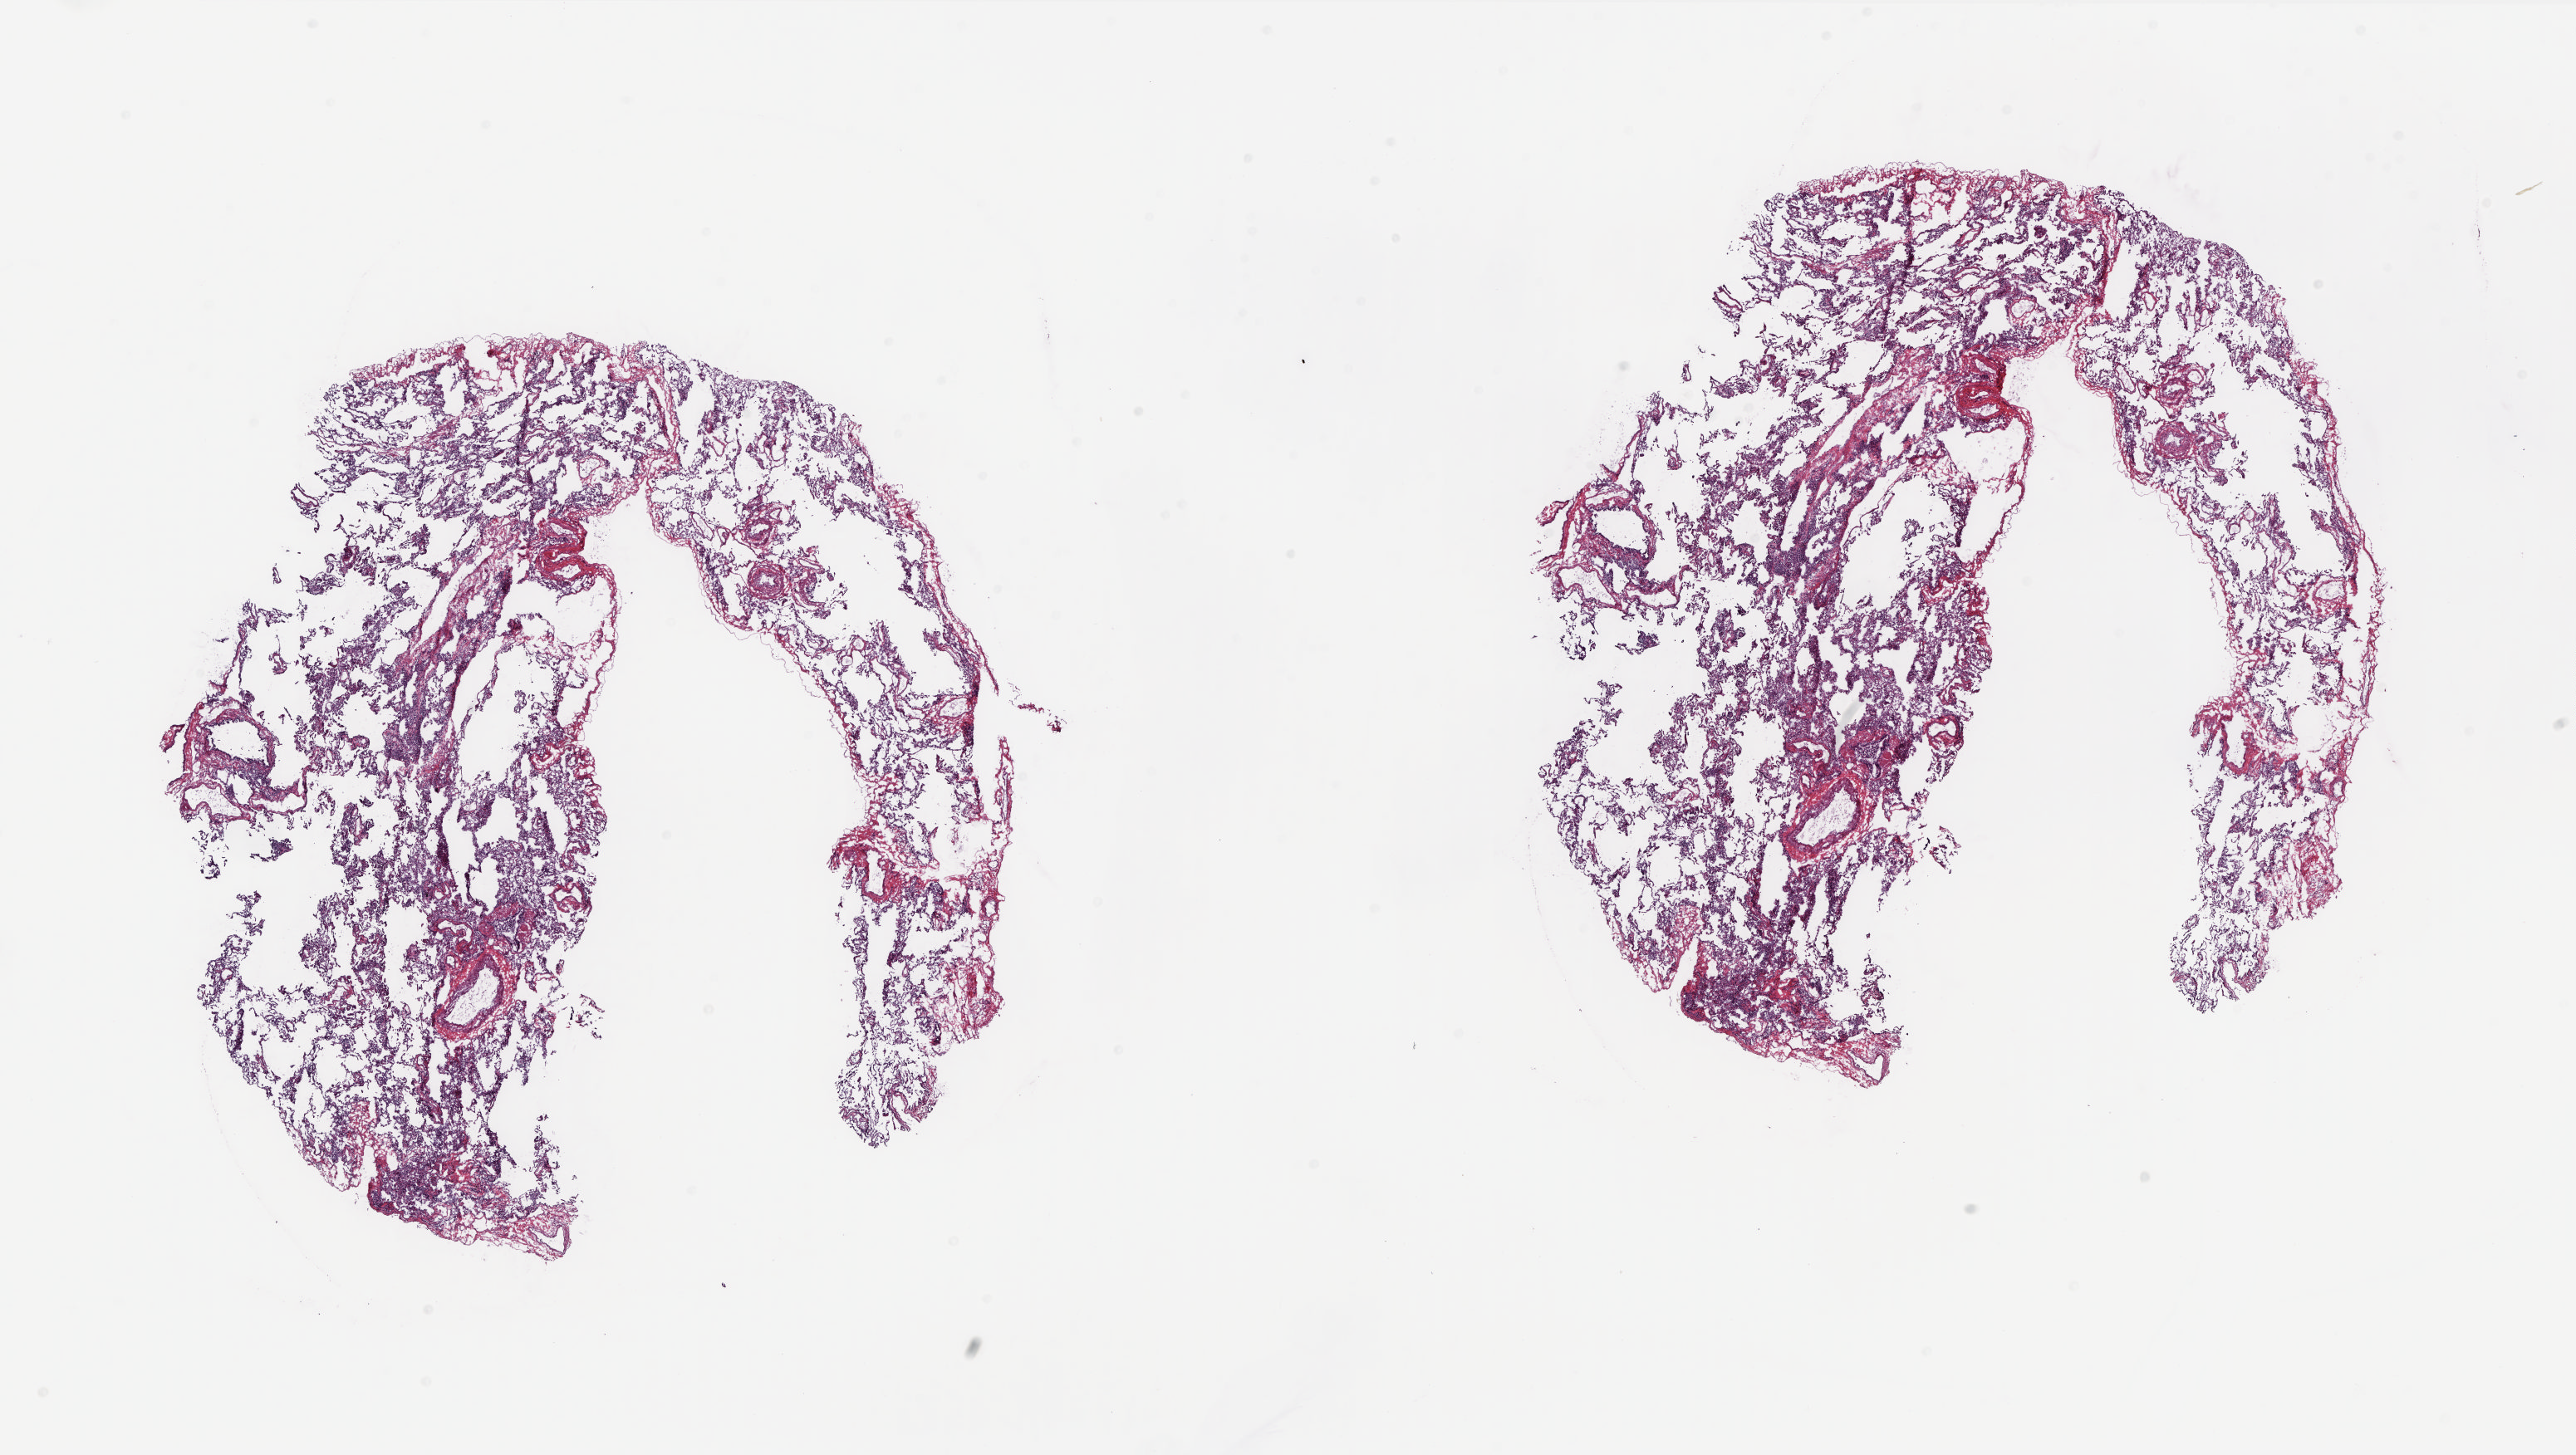
Whole-slide histology image, H&E — a low-resolution overview of the entire scanned area, about 25.0 x 14.1 mm; frozen section; solid tissue normal (non-tumour tissue) sample from the lung. Male patient; age at initial diagnosis 64 years. Composition of this section per pathologist review: tumour cells 0%, tumour nuclei 0%, normal cells 100%, stromal cells 0%, necrosis 0%. Infiltration values recorded for this section: lymphocyte infiltration 20%, monocyte infiltration 20%, neutrophil infiltration 40%.
* this section: solid tissue normal (non-tumour) sample from the same patient
* patient diagnosis: Mucinous adenocarcinoma (lower lobe, lung)